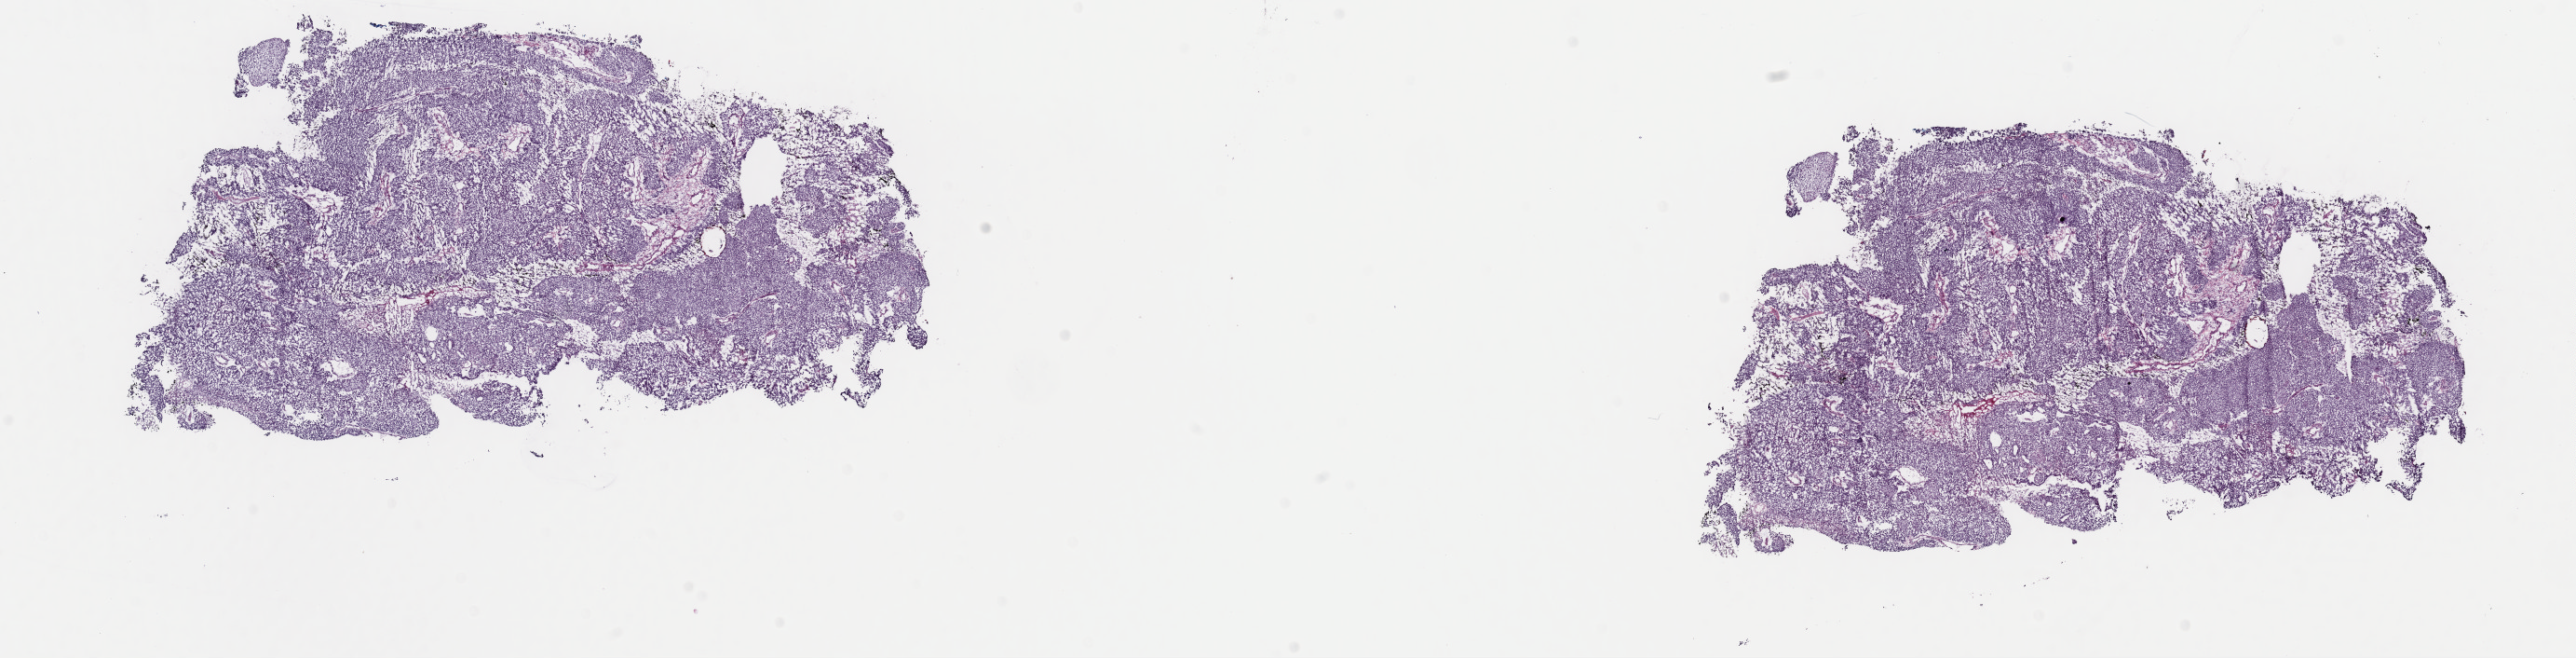
Whole-slide histology image, H&E — low-resolution overview of the scanned area, about 21.9 x 5.6 mm (from a 40x scan); frozen section from the top of the tissue portion; primary tumour sample from the uterus. Female, age 55 years at initial diagnosis. Histologic grade: G3 (poorly differentiated). Composition of this section per pathologist review: tumour cells 97%, tumour nuclei 90%, normal cells 0%, stromal cells 0%, necrosis 3%. Infiltration values recorded for this section: lymphocyte infiltration 3%, monocyte infiltration 0%, neutrophil infiltration 0%.
* FIGO stage: IIIA
* pathologic diagnosis: Endometrioid adenocarcinoma, NOS